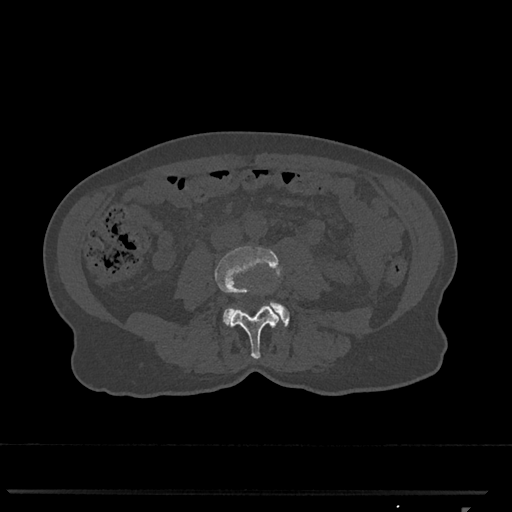
CT including the spine, one axial slice. Position 250 of 793 along the scan axis. 120 kVp. Bone window (W 1800 / L 400 HU). 0.5 mm slice thickness. 512 × 512 image matrix, field of view 380 × 380 mm. Female patient, age 62 years. From the clinical record (not read from this slice): primary cancer: renal.
Outlined on this slice (semi-automatically segmented with operator editing):
- L3 vertebra: bounding box [x1, y1, x2, y2] px = [214, 246, 282, 359]
- L4 vertebra: [223, 301, 290, 327]